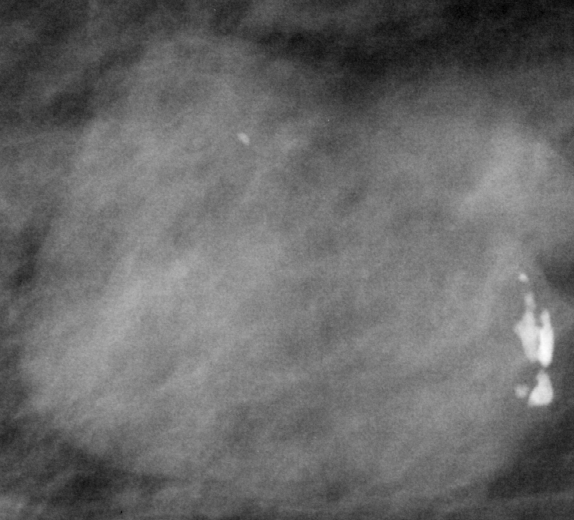
Region of interest cut from a scanned film mammogram (one marked finding), right breast, MLO view.
Marked abnormality: mass, shape lobulated, margins circumscribed; BI-RADS assessment category 3; pathology (as recorded): benign.